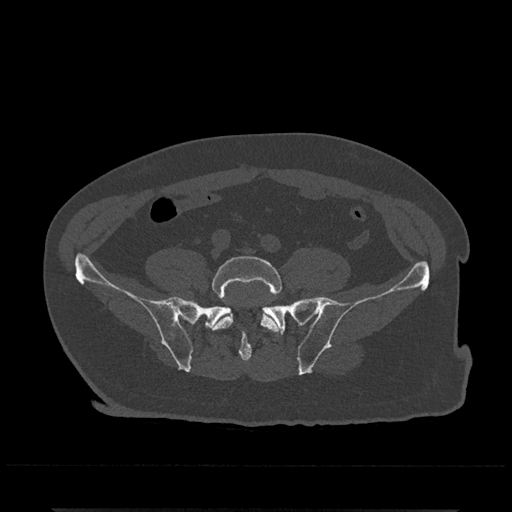
CT including the spine, one axial slice; 120 kVp; bone window (W 1800 / L 400 HU); 512 × 512 image matrix. Male patient, age 67 years. Case-level facts recorded for this patient, not image findings: primary cancer: prostate.
Annotated regions visible in this slice (semi-automatically segmented with operator editing):
- L5 vertebra: bounding box <209,256,282,332> (left, top, right, bottom; pixels)